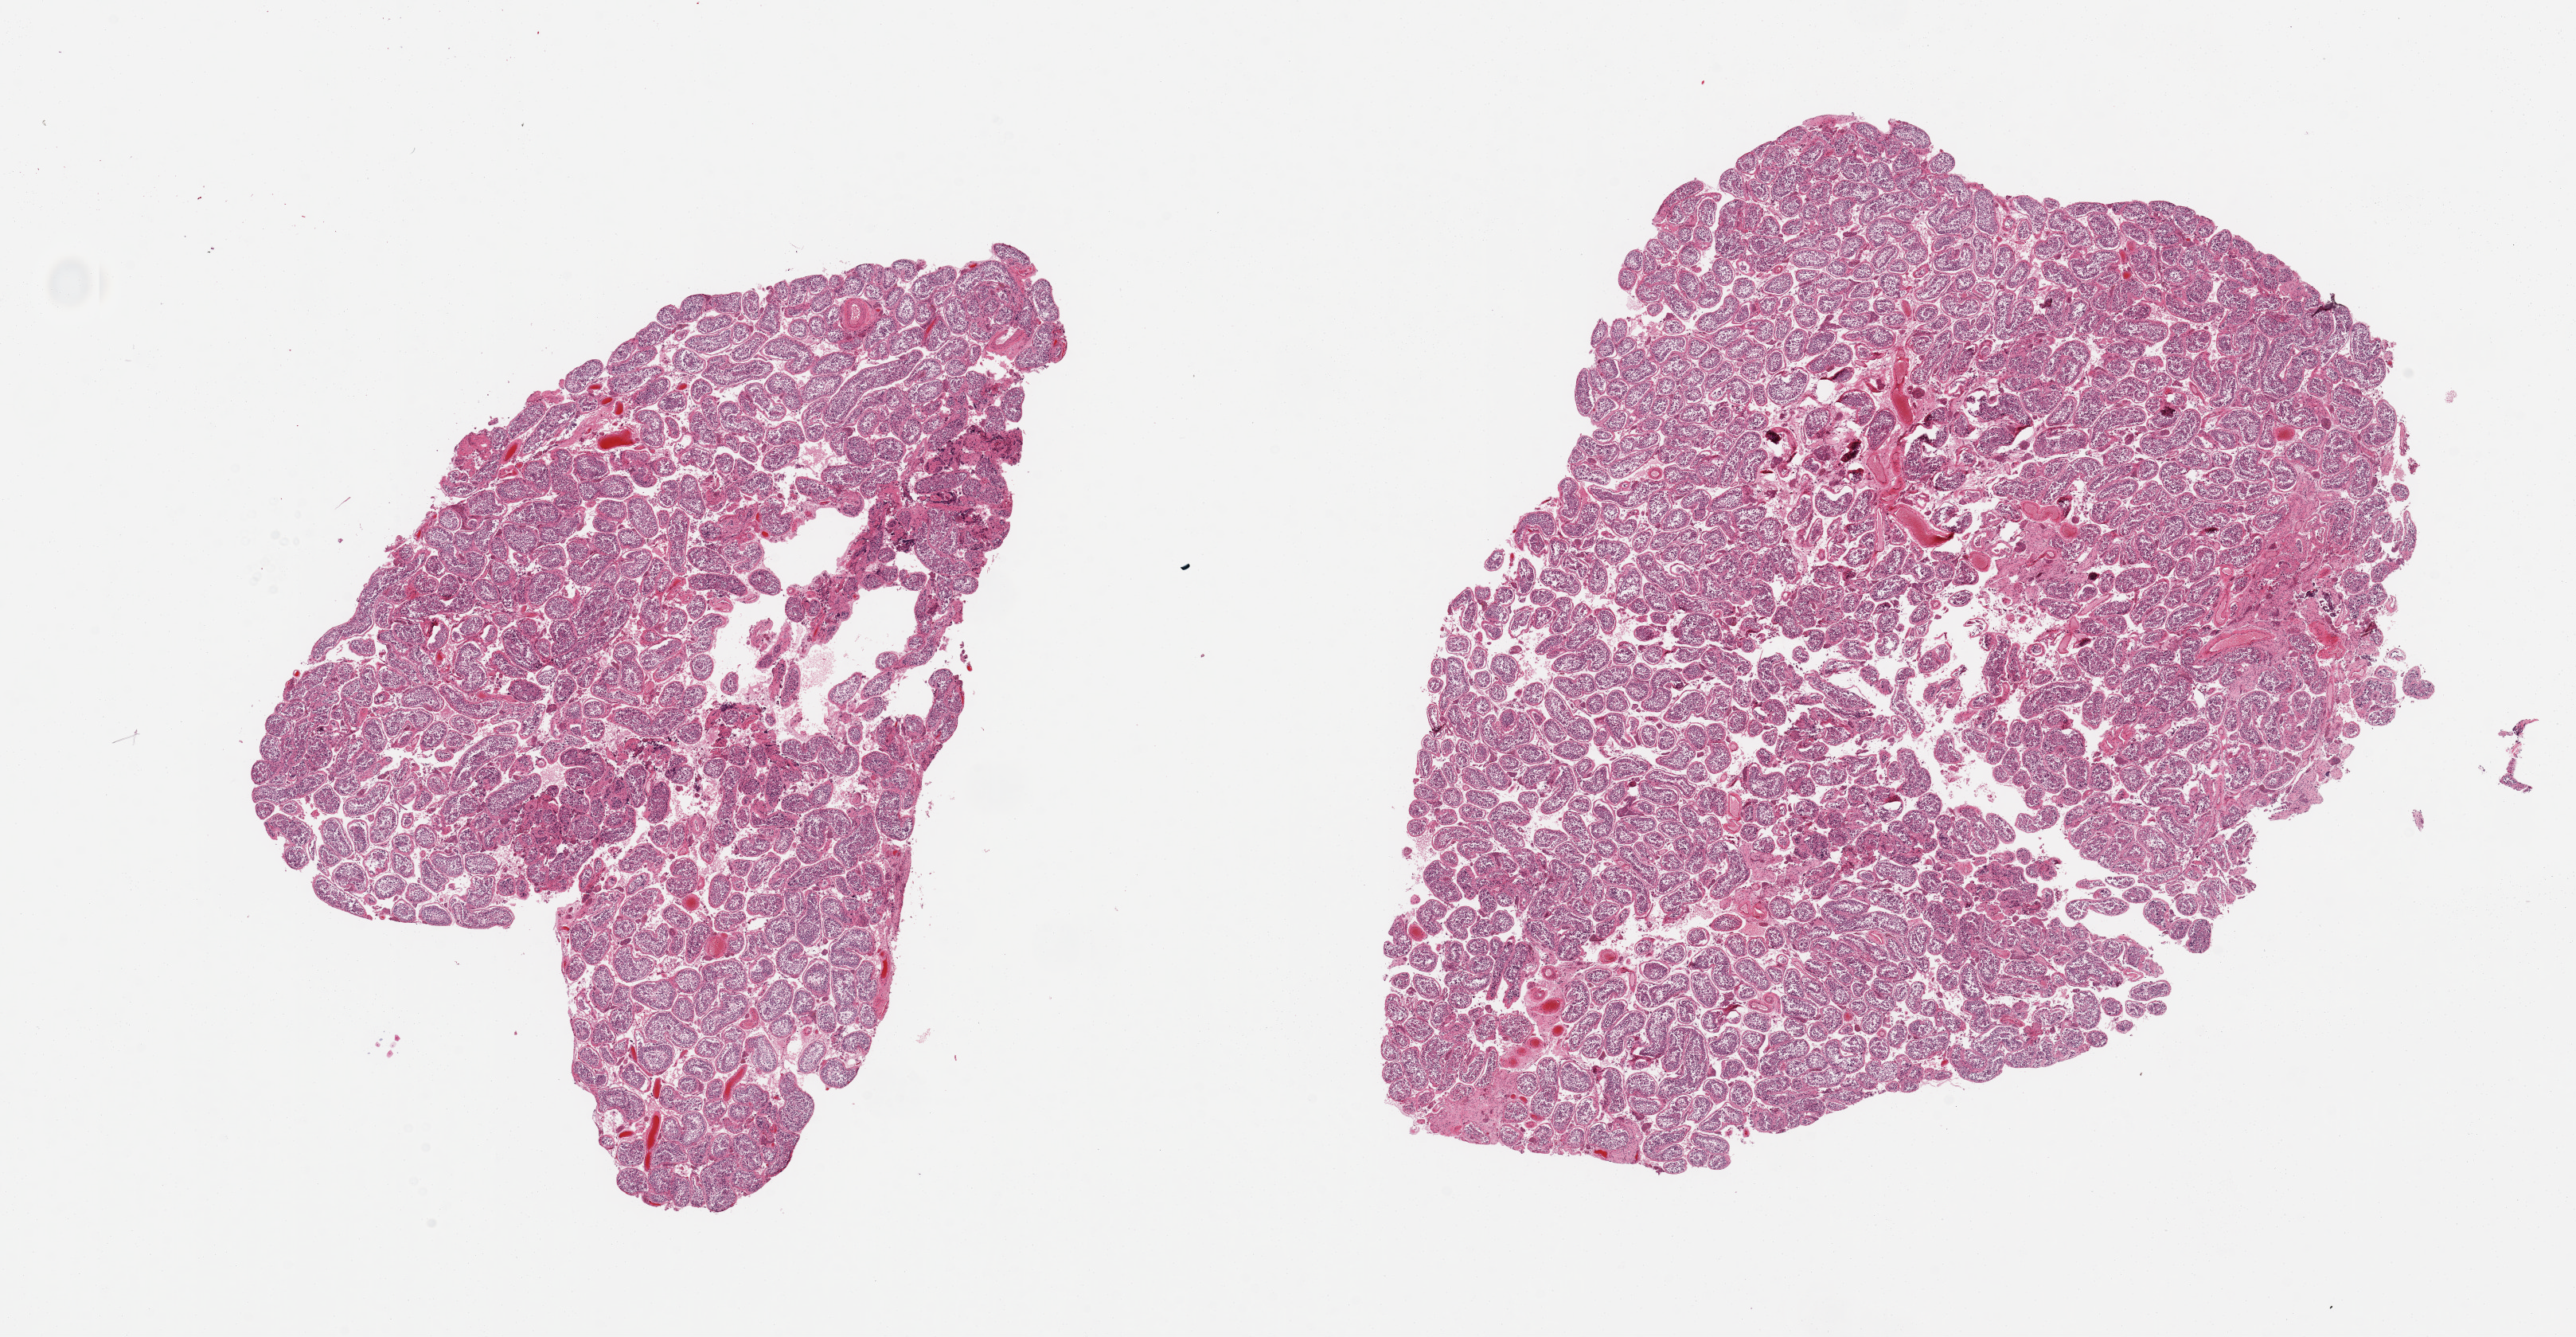
Hematoxylin and eosin (H&E) whole-slide image — whole scanned area (about 25.6 x 13.3 mm, slide scanned at 20x) shown as a low-resolution overview, PAXgene-fixed paraffin-embedded (PFPE) section, target tissue: testis, donor tissue sample.
- review note (as recorded): 2 pieces; spermatogenesis is present, rare hyalinized tubules